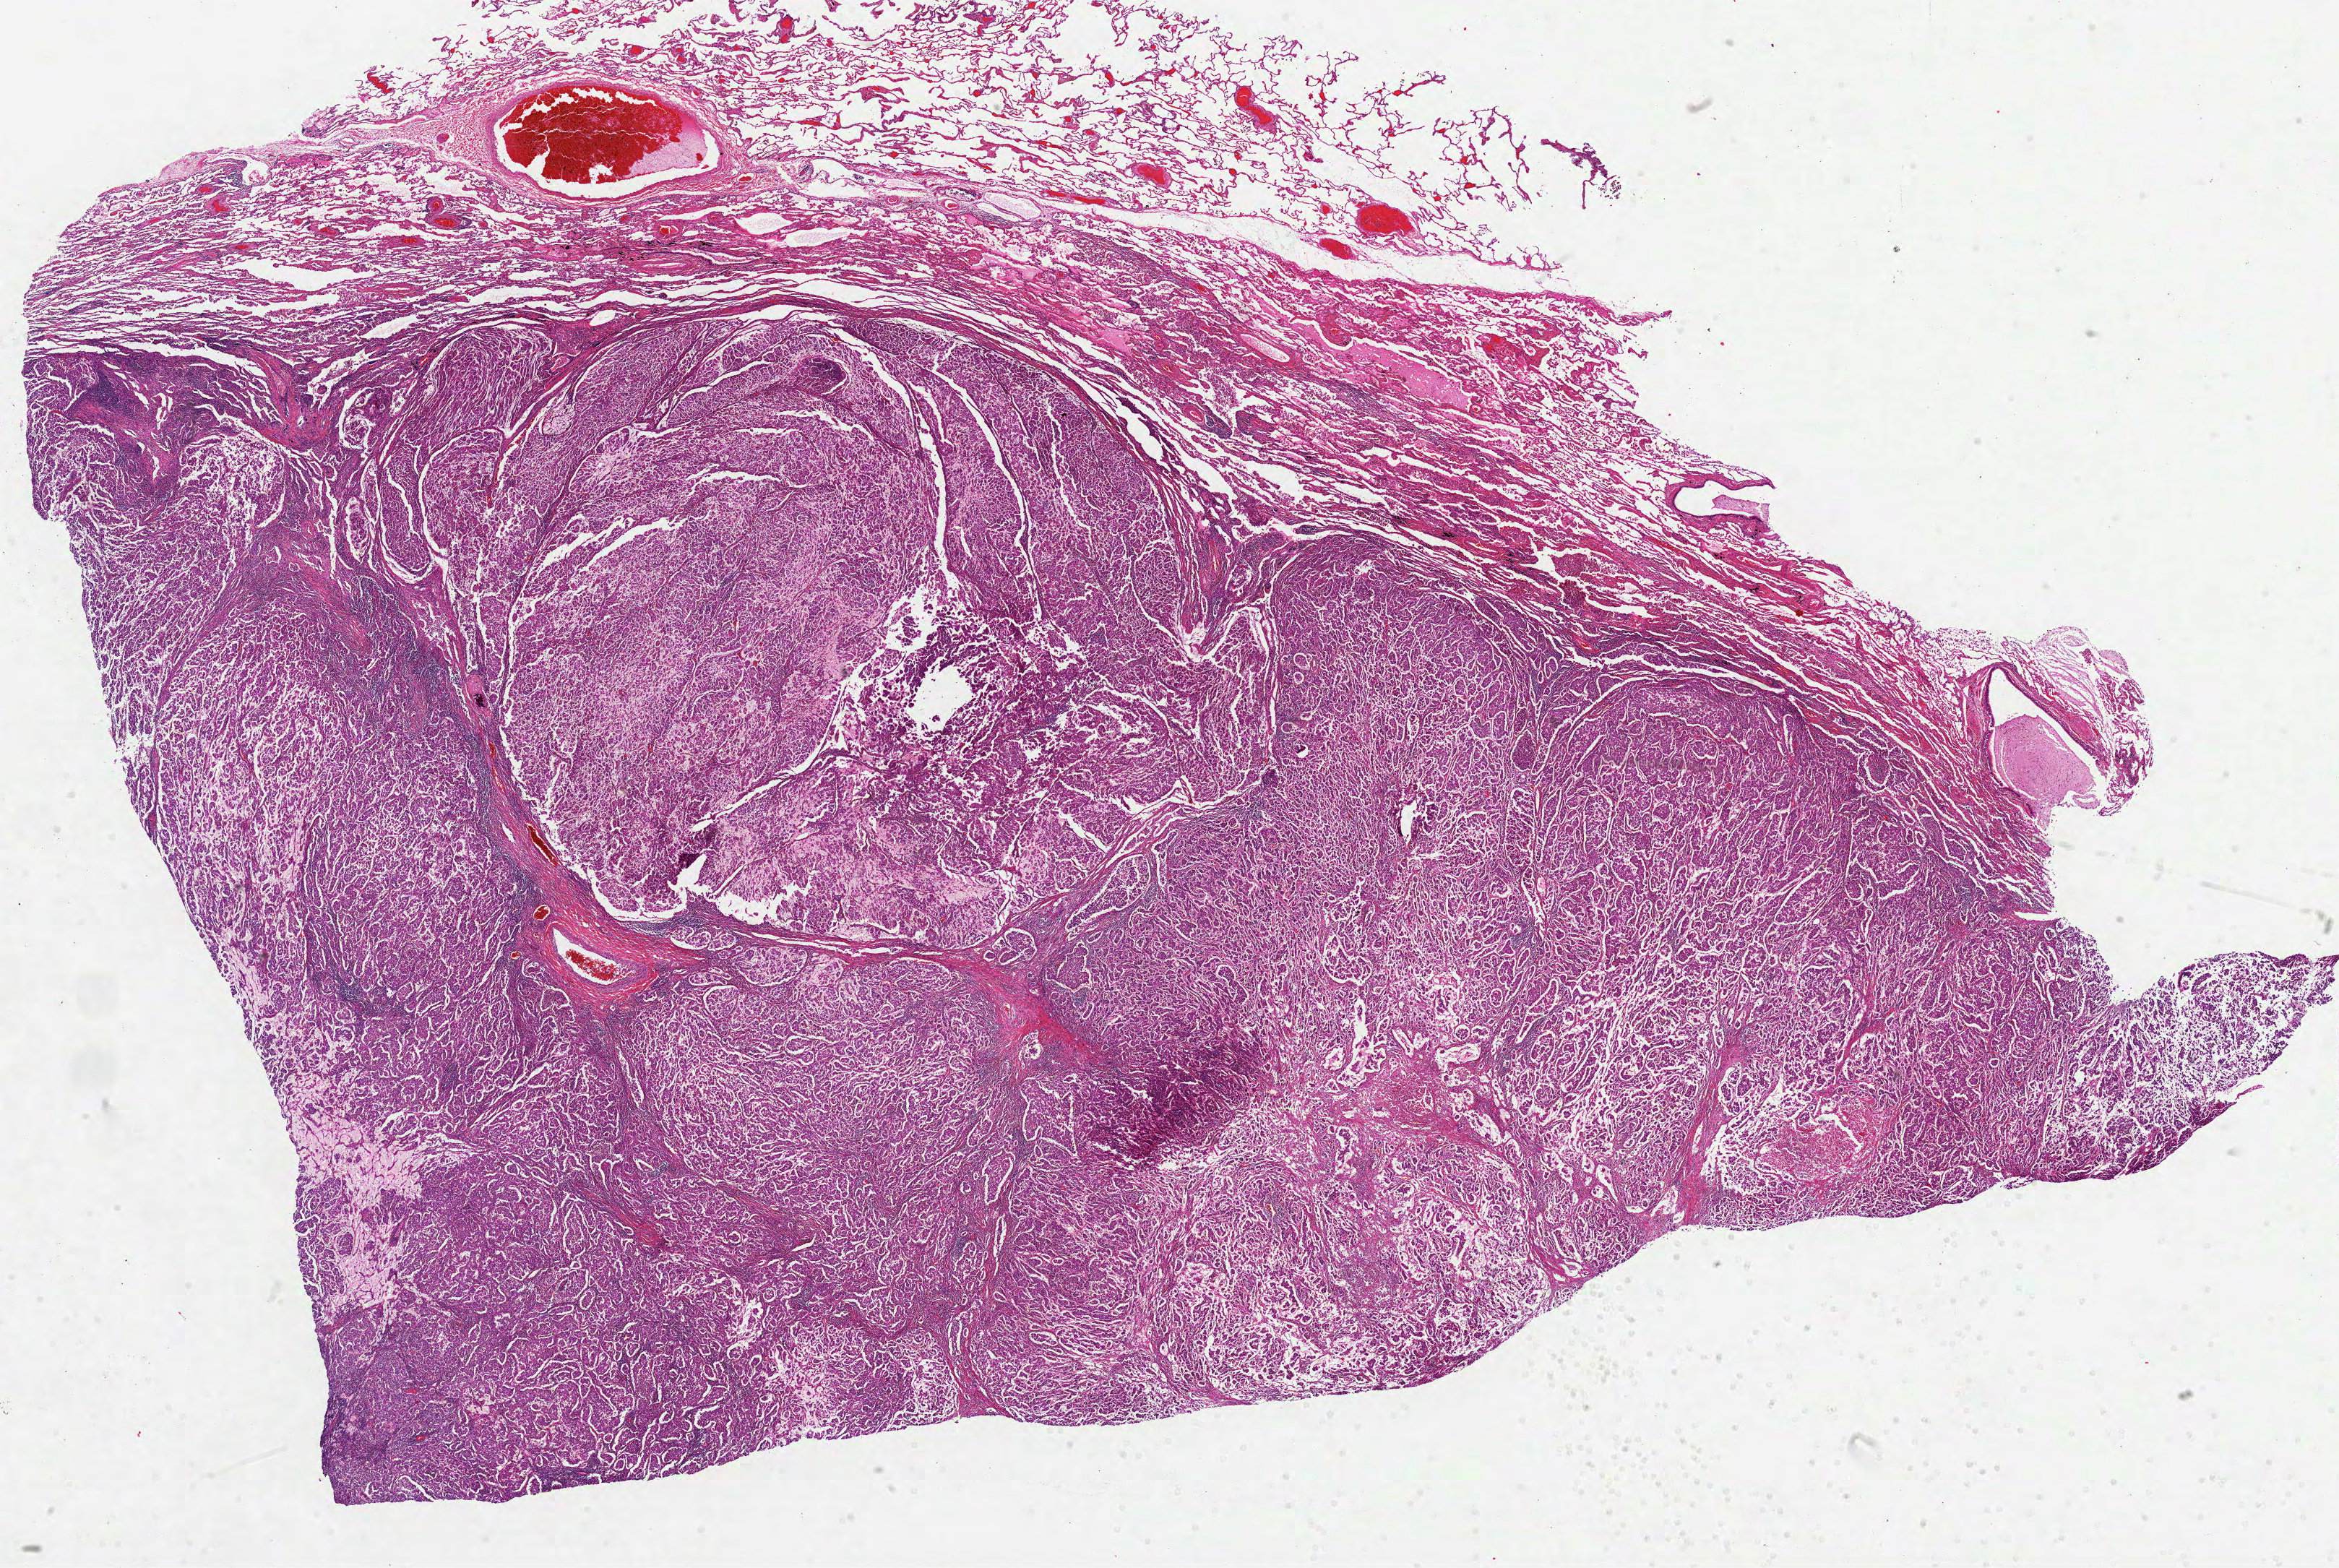
Hematoxylin and eosin (H&E) stained whole-slide image — a low-resolution overview of the entire scanned area, about 26.1 x 17.5 mm (from a 40x scan). Formalin-fixed paraffin-embedded (FFPE) diagnostic section. Lung, primary tumour sample. Female, age 68 years at initial diagnosis.
* diagnosis: Adenocarcinoma, NOS (upper lobe, lung)
* AJCC pathologic stage: IIB (4th edition)
* TNM: T2 N1 M0